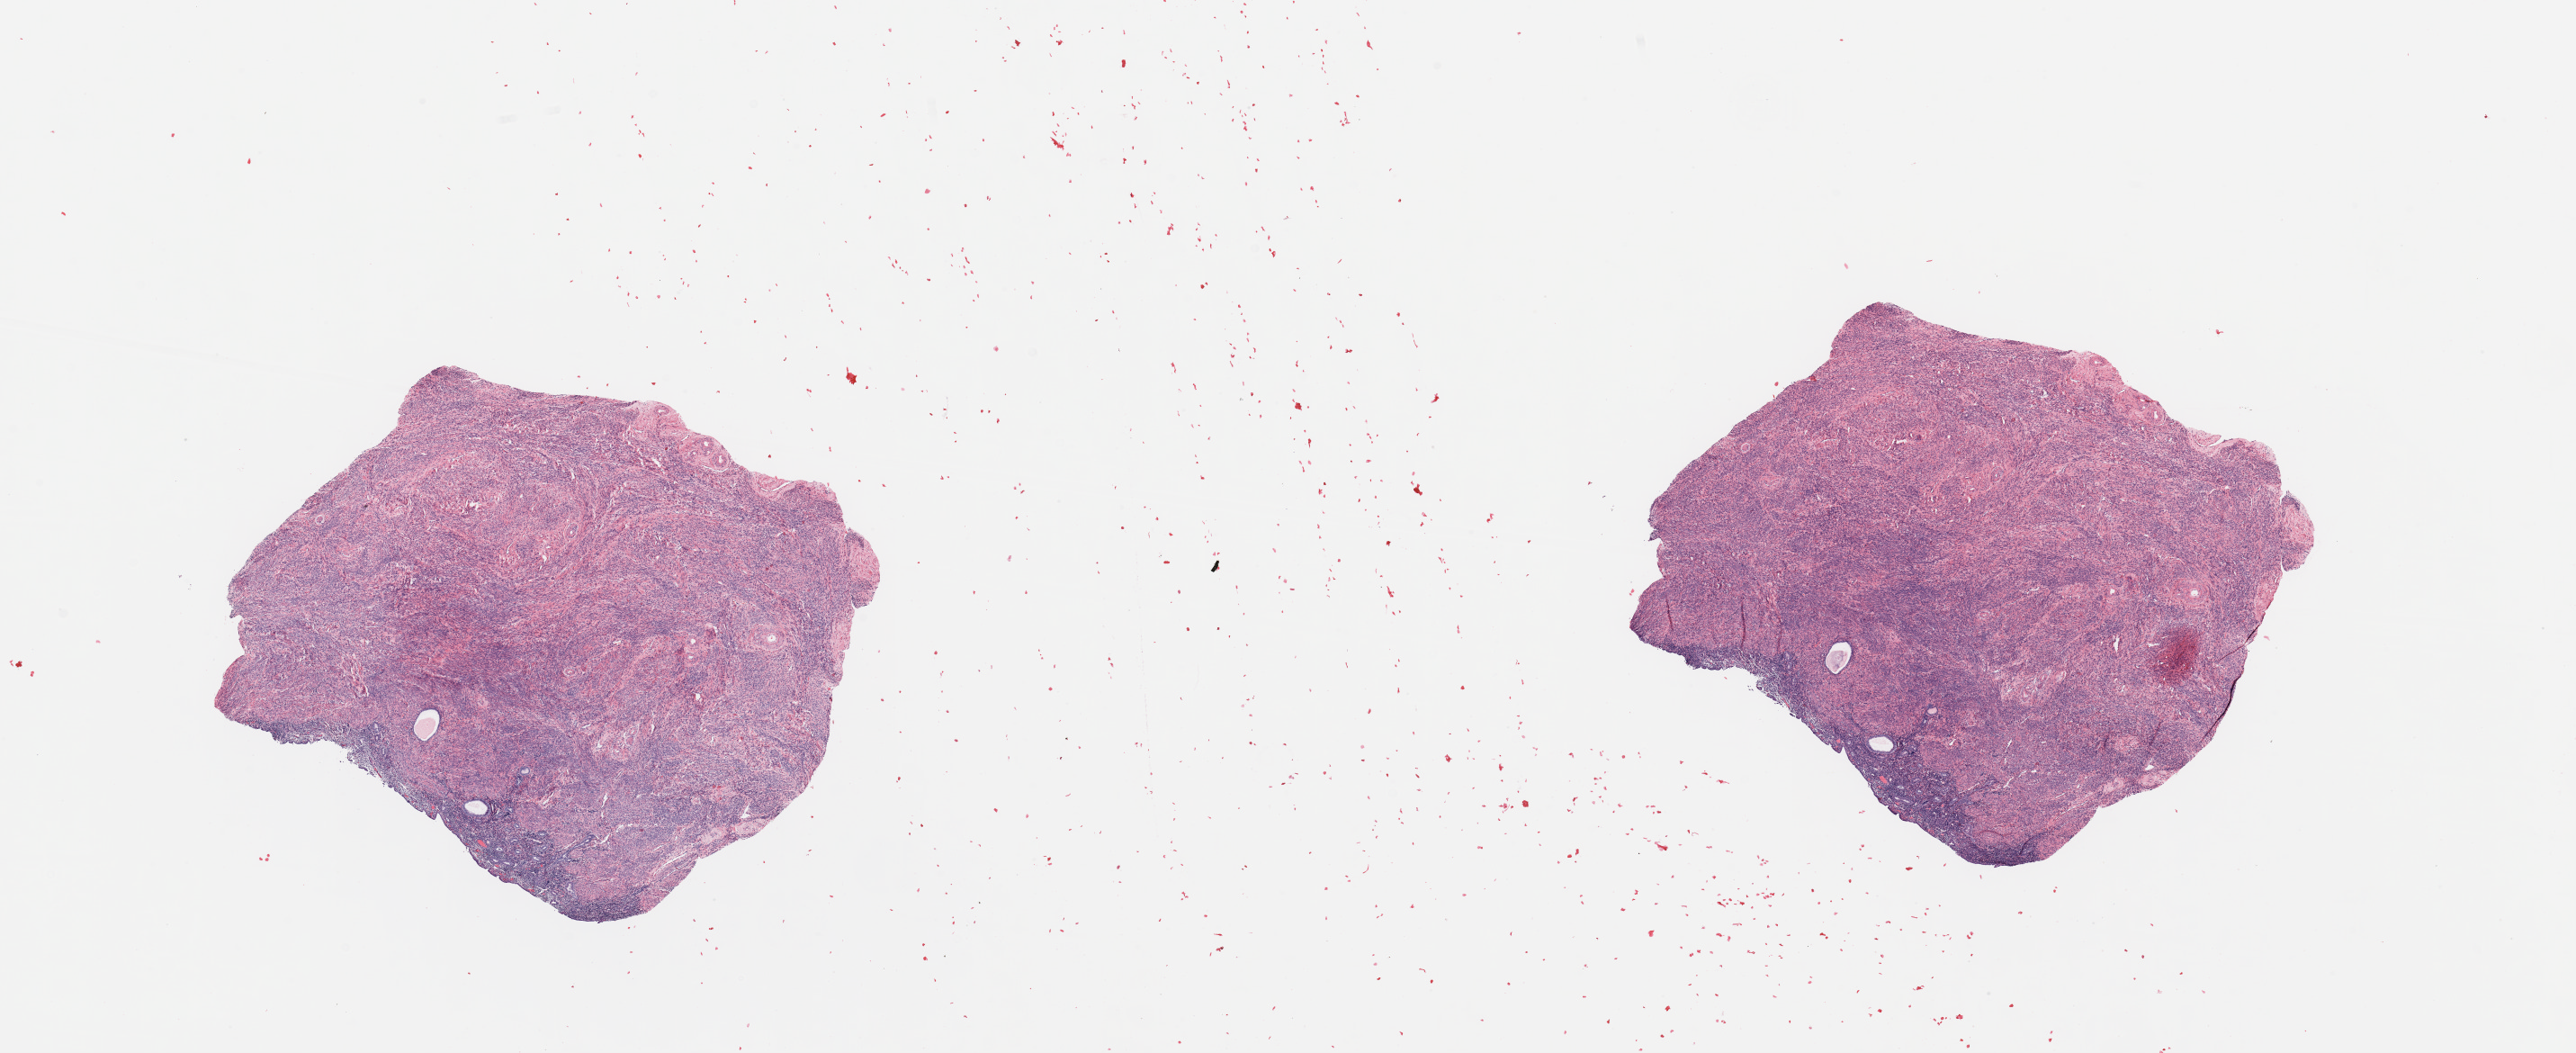
Hematoxylin and eosin (H&E) stained whole-slide image — whole scanned area (about 22.6 x 9.3 mm) shown as a low-resolution overview; normal (non-tumour) tissue sample, sampled site: uterus. Female, 77 y/o.
* this section: normal (non-tumour) tissue from the same patient
* patient diagnosis: Endometrioid adenocarcinoma, NOS